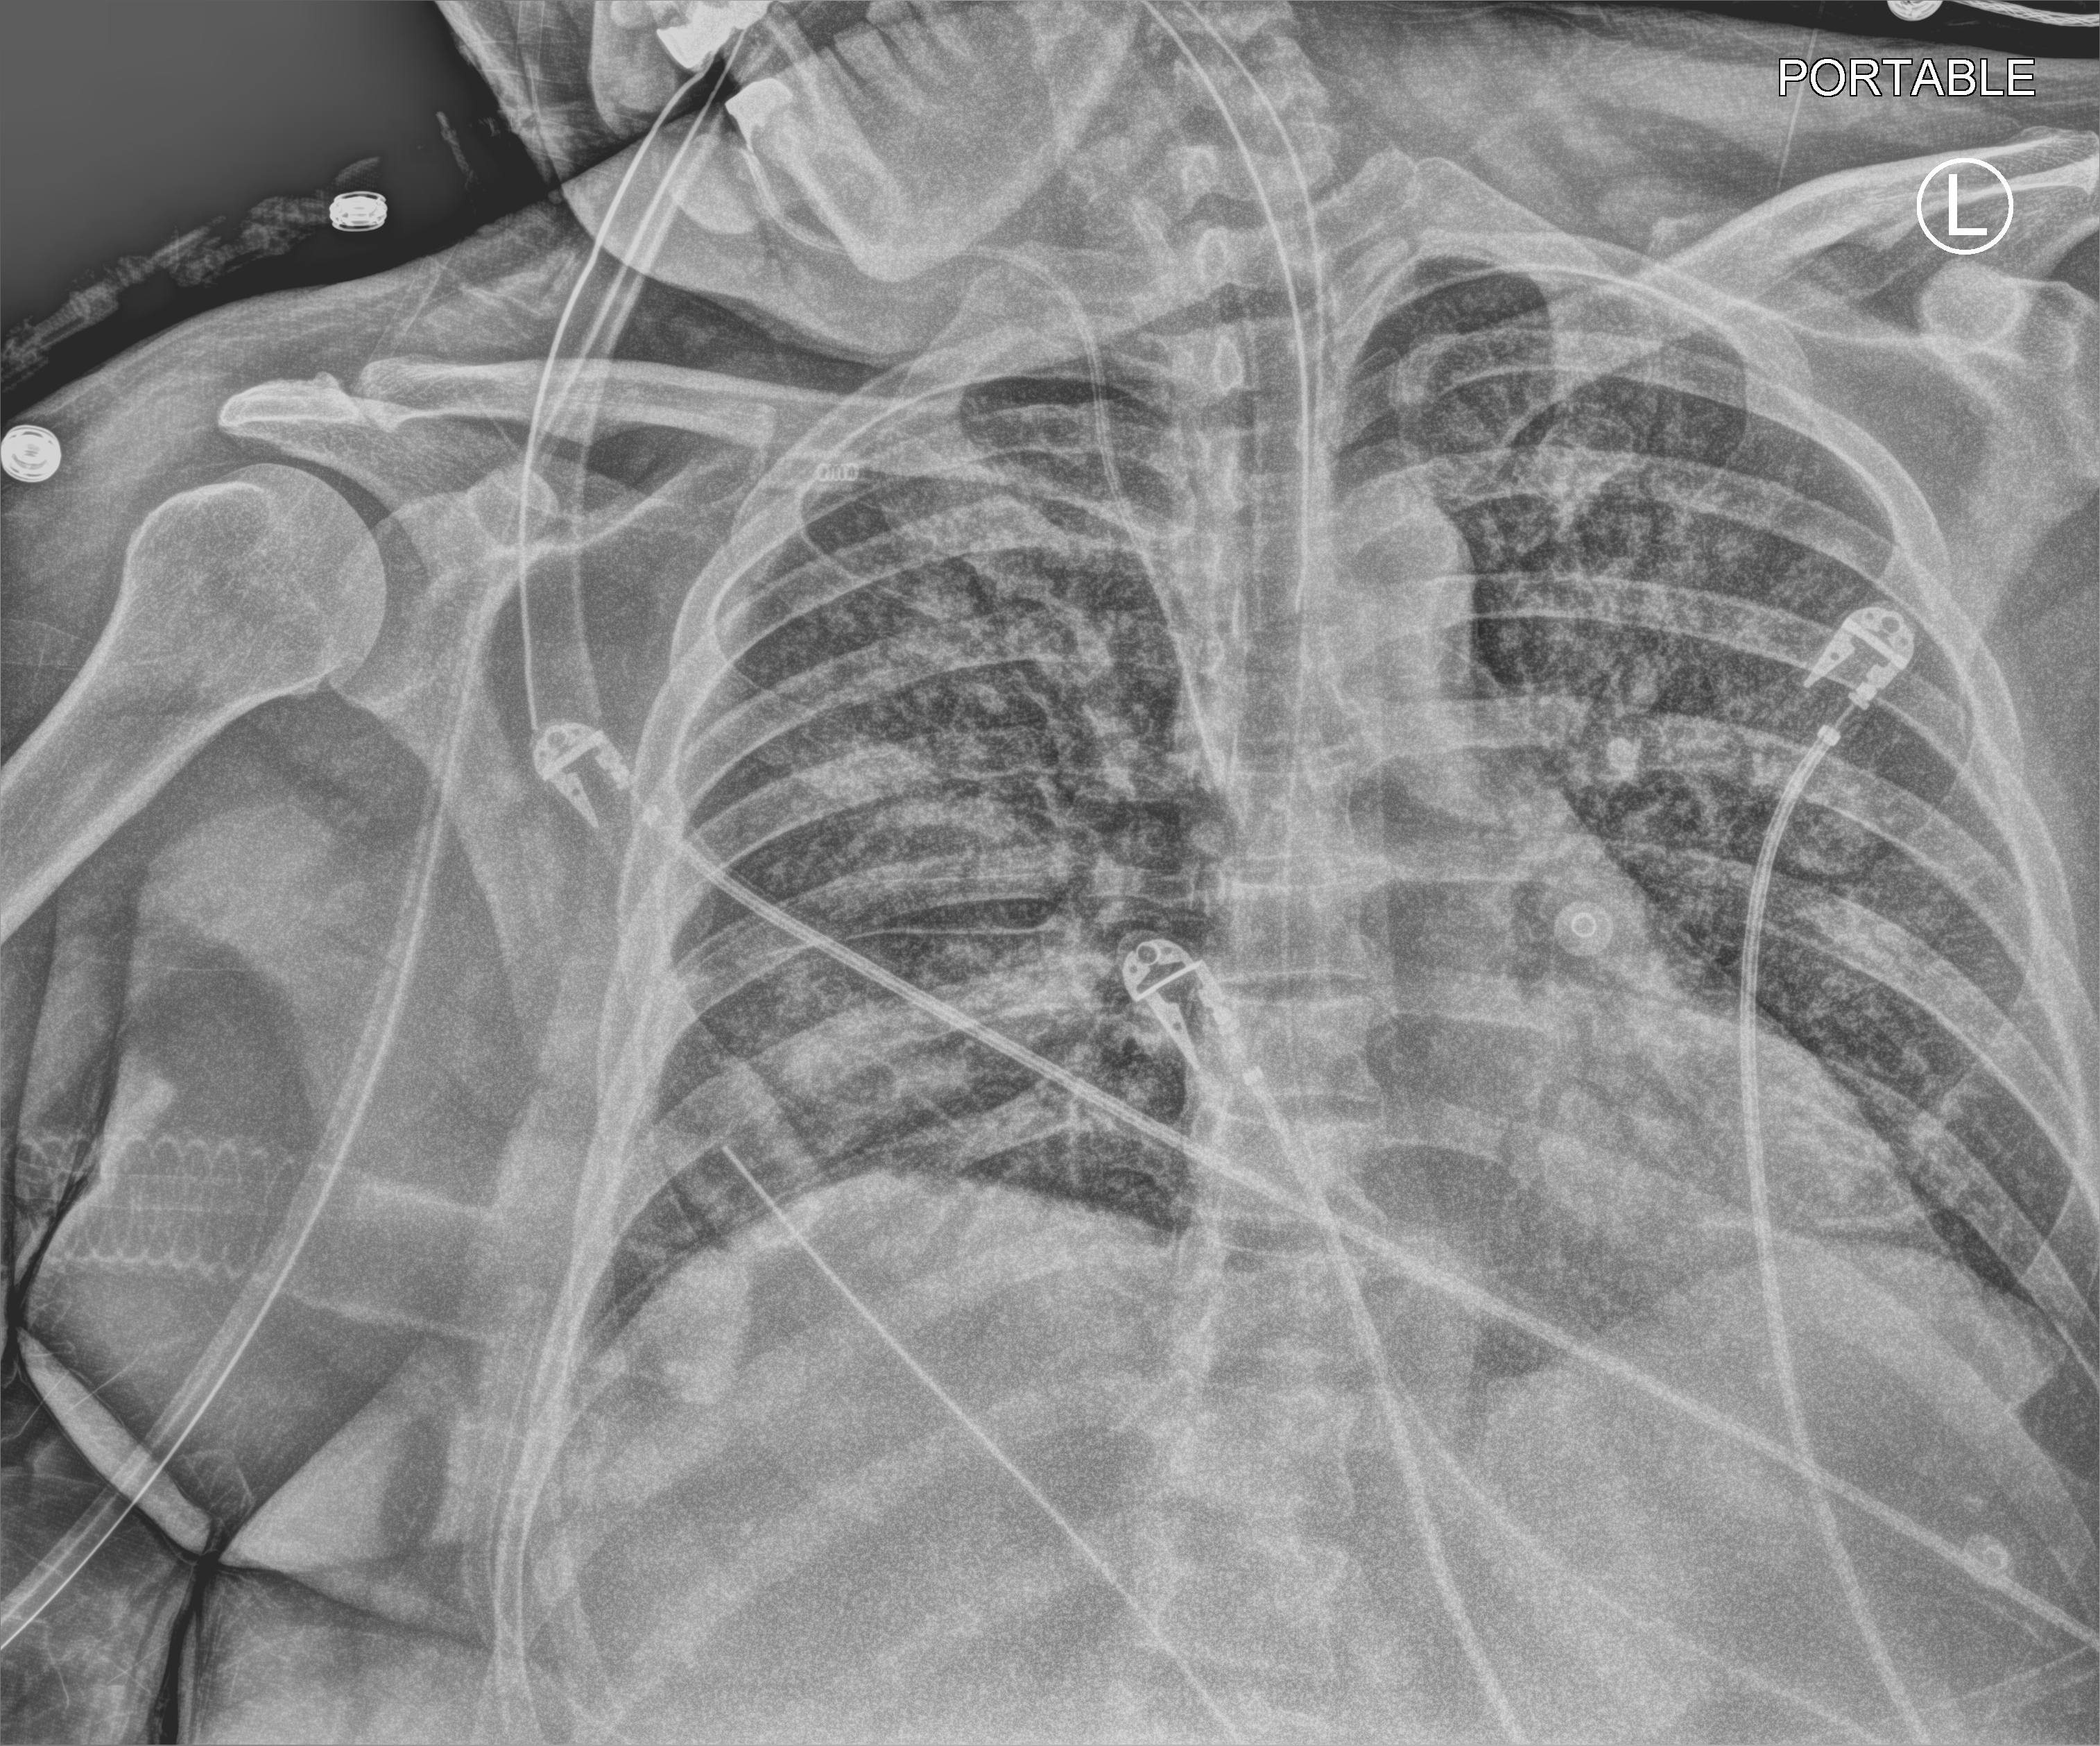
Bedside chest radiograph (computed radiography). Patient hospitalised with COVID-19; male, aged 18–59 years.
From the hospital-stay record, not from the radiograph (when in the stay this image was taken is not recorded): admitted to intensive care during this hospital stay: yes.